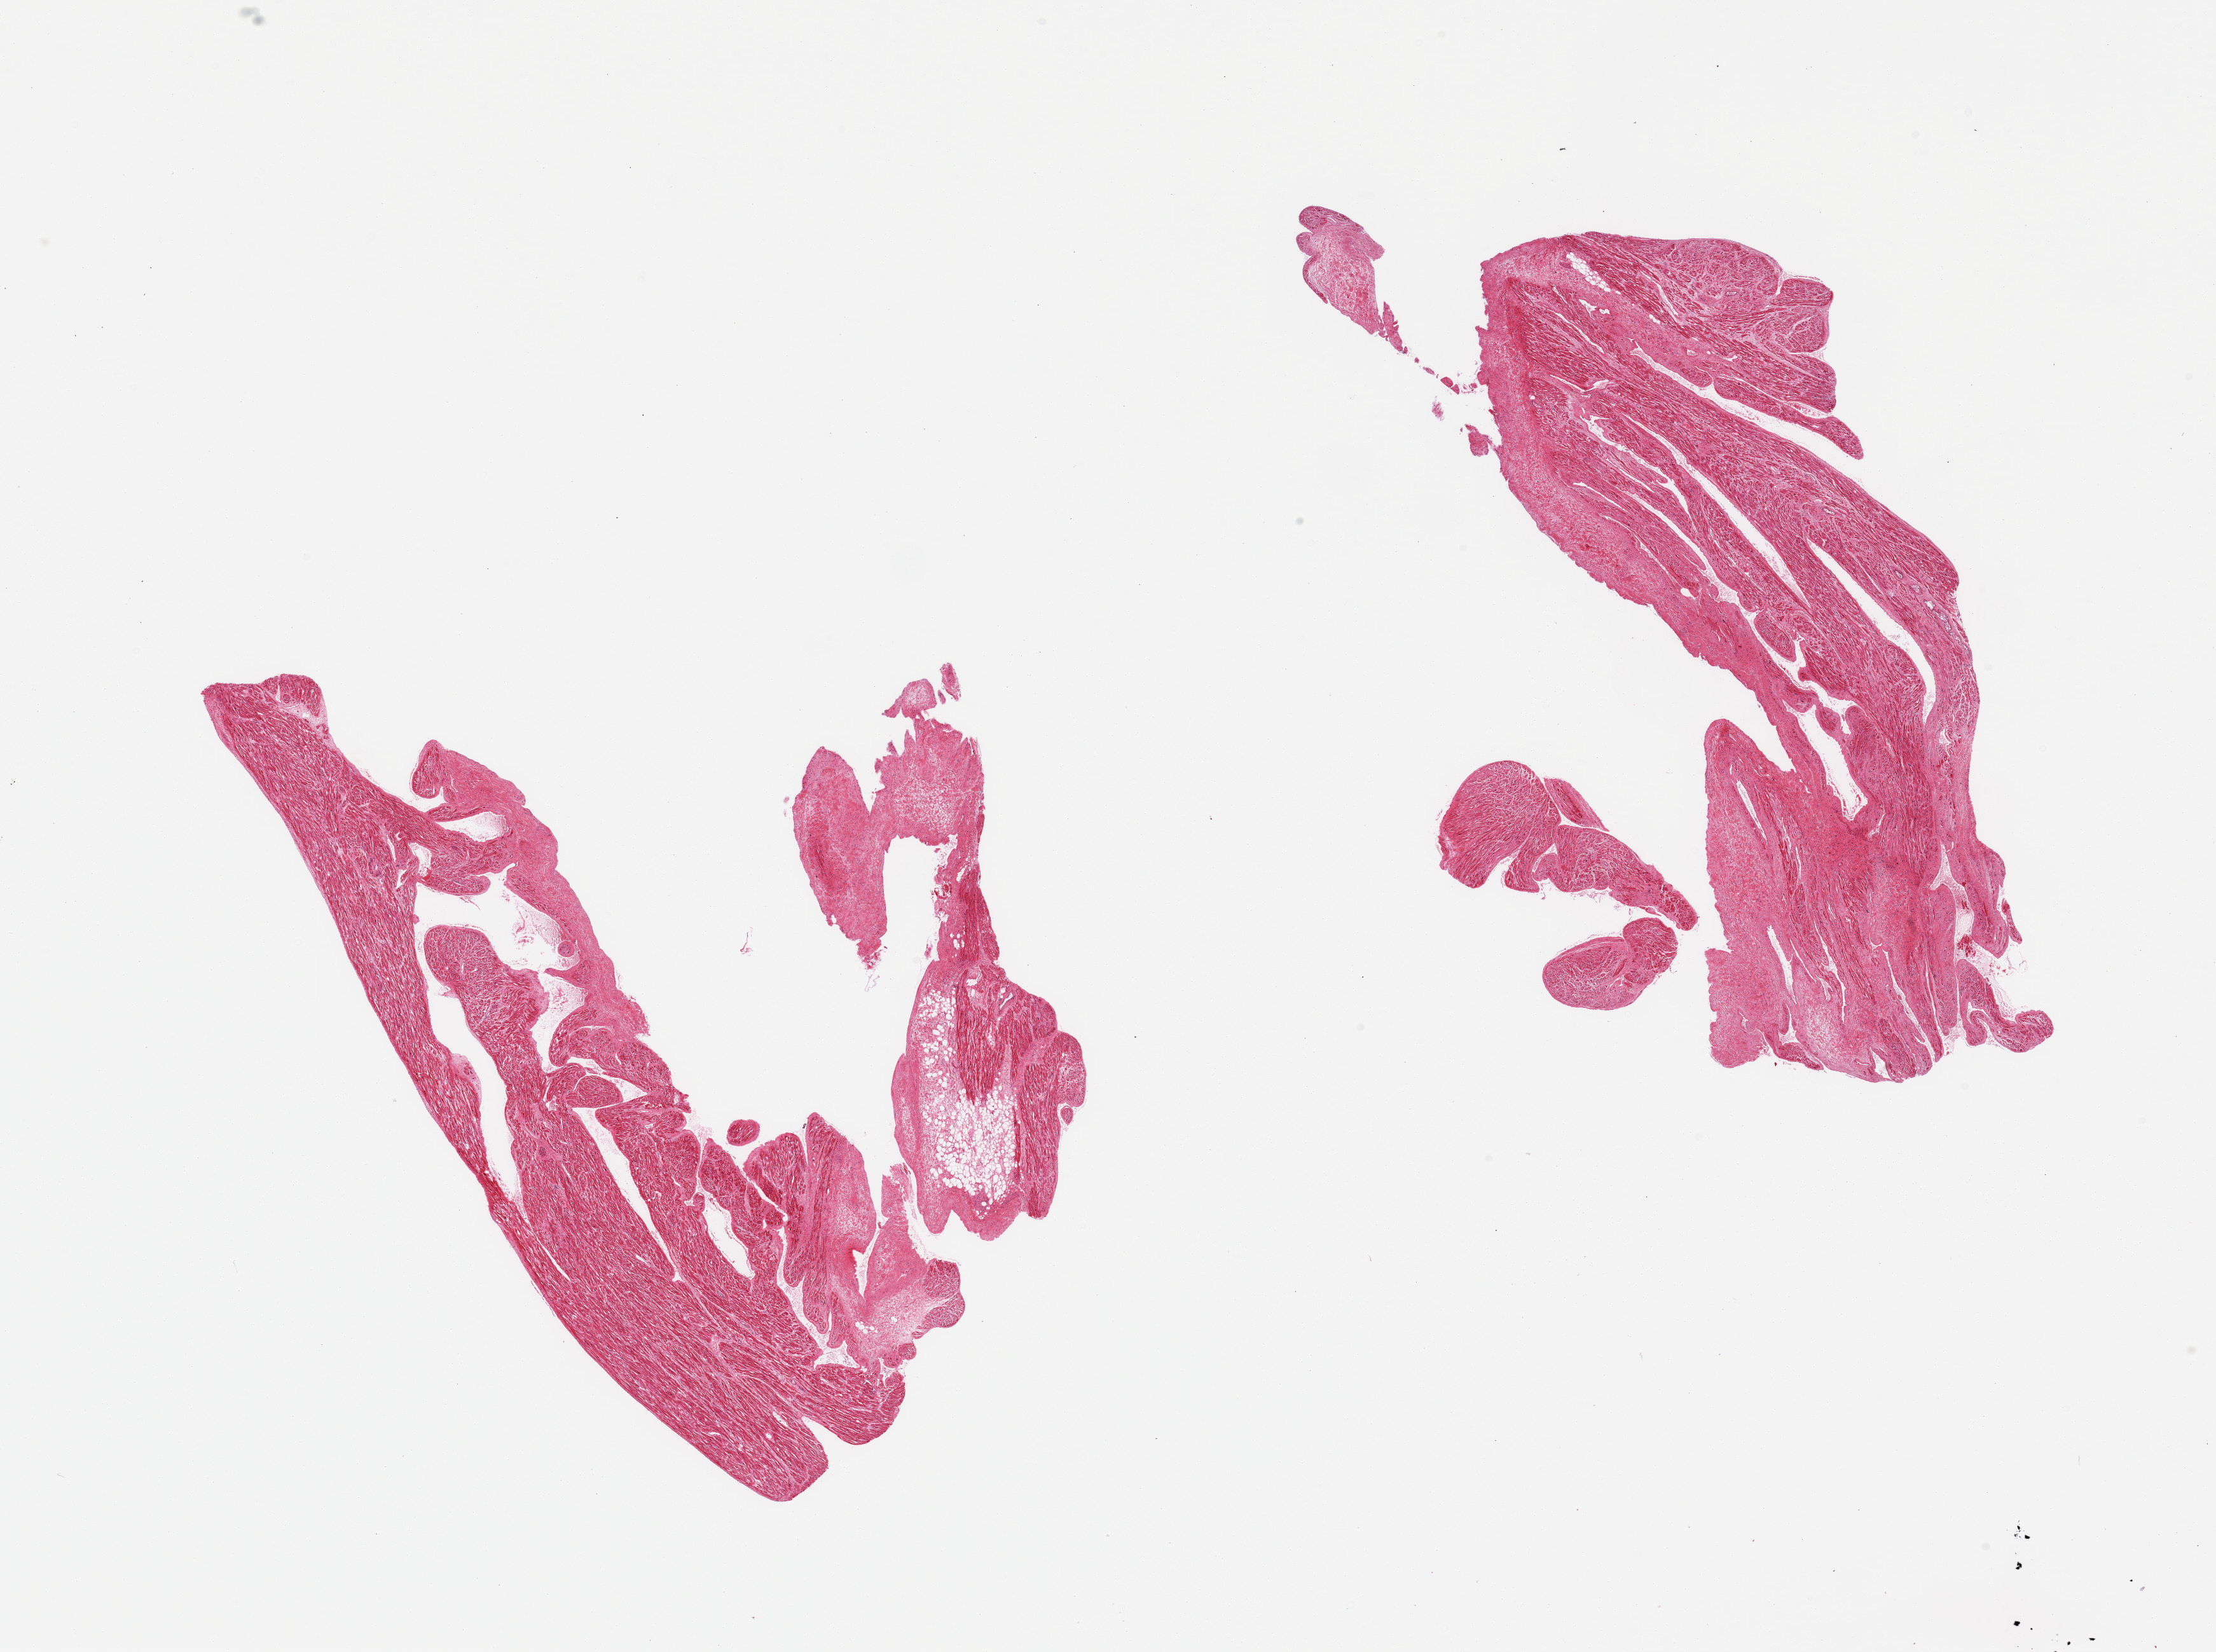
H&E whole-slide image, whole scanned area (about 27.6 x 20.5 mm) shown as a low-resolution overview. PAXgene-fixed paraffin-embedded (PFPE) section. Target tissue: auricular appendage. Donor tissue sample. Donor: male.
* review note (as recorded): 2 pieces; mild fibrosis and focal accumulation of internal fat